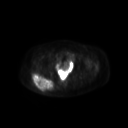
FDG PET of an extremity soft-tissue mass (from a PET/CT study), one axial slice; slice 52 of 267 in the series (ordered by position); 3.27 mm slice thickness; 128 × 128 image matrix, field of view 600 × 600 mm. Patient: female, 60 years. Case-level facts recorded for this patient, not image findings: histological type: spindle cell suggestive of myxofibrosarcoma; grade: intermediate; site of the primary tumour: right buttock.
Annotated regions visible in this slice (expert contour drawn on MRI and transferred to this co-registered scan by the dataset authors):
- gross tumour volume (mass): box from (x=32, y=72) to (x=55, y=92) px